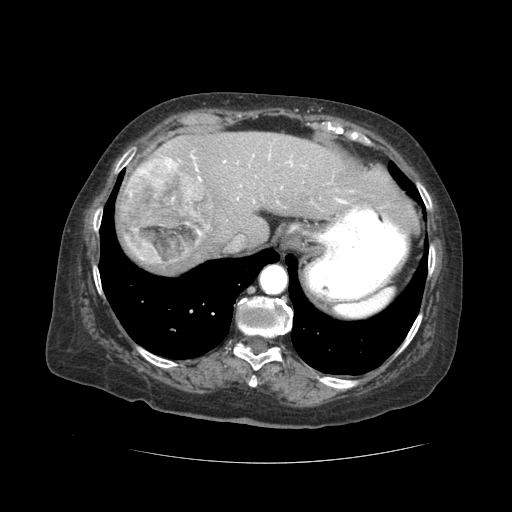
Contrast-enhanced abdominal CT (liver protocol), one axial slice; slice 37 of 59 in the series (ordered by position); 120 kVp; soft-tissue window (W 400 / L 40 HU); 512 × 512 image matrix, field of view 380 × 380 mm. Case-level facts recorded for this patient, not image findings: diagnosis: hepatocellular carcinoma (patient treated with transarterial chemoembolisation; whether this scan precedes or follows treatment is not stated here); TNM stage (as recorded): Stage-I; Child-Pugh class: A; tumour nodularity: uninodular.
Annotated regions visible in this slice (semi-automatic segmentation, software-assisted and operator-edited):
- abdominal aorta: bounding box <261,266,286,293> (left, top, right, bottom; pixels)
- liver parenchyma outside the tumour (the mass and vessels are separate outlines, so this box may not span the whole liver): <118,132,414,272>
- mass: <122,155,213,263>
- liver vessels: <191,154,387,220>